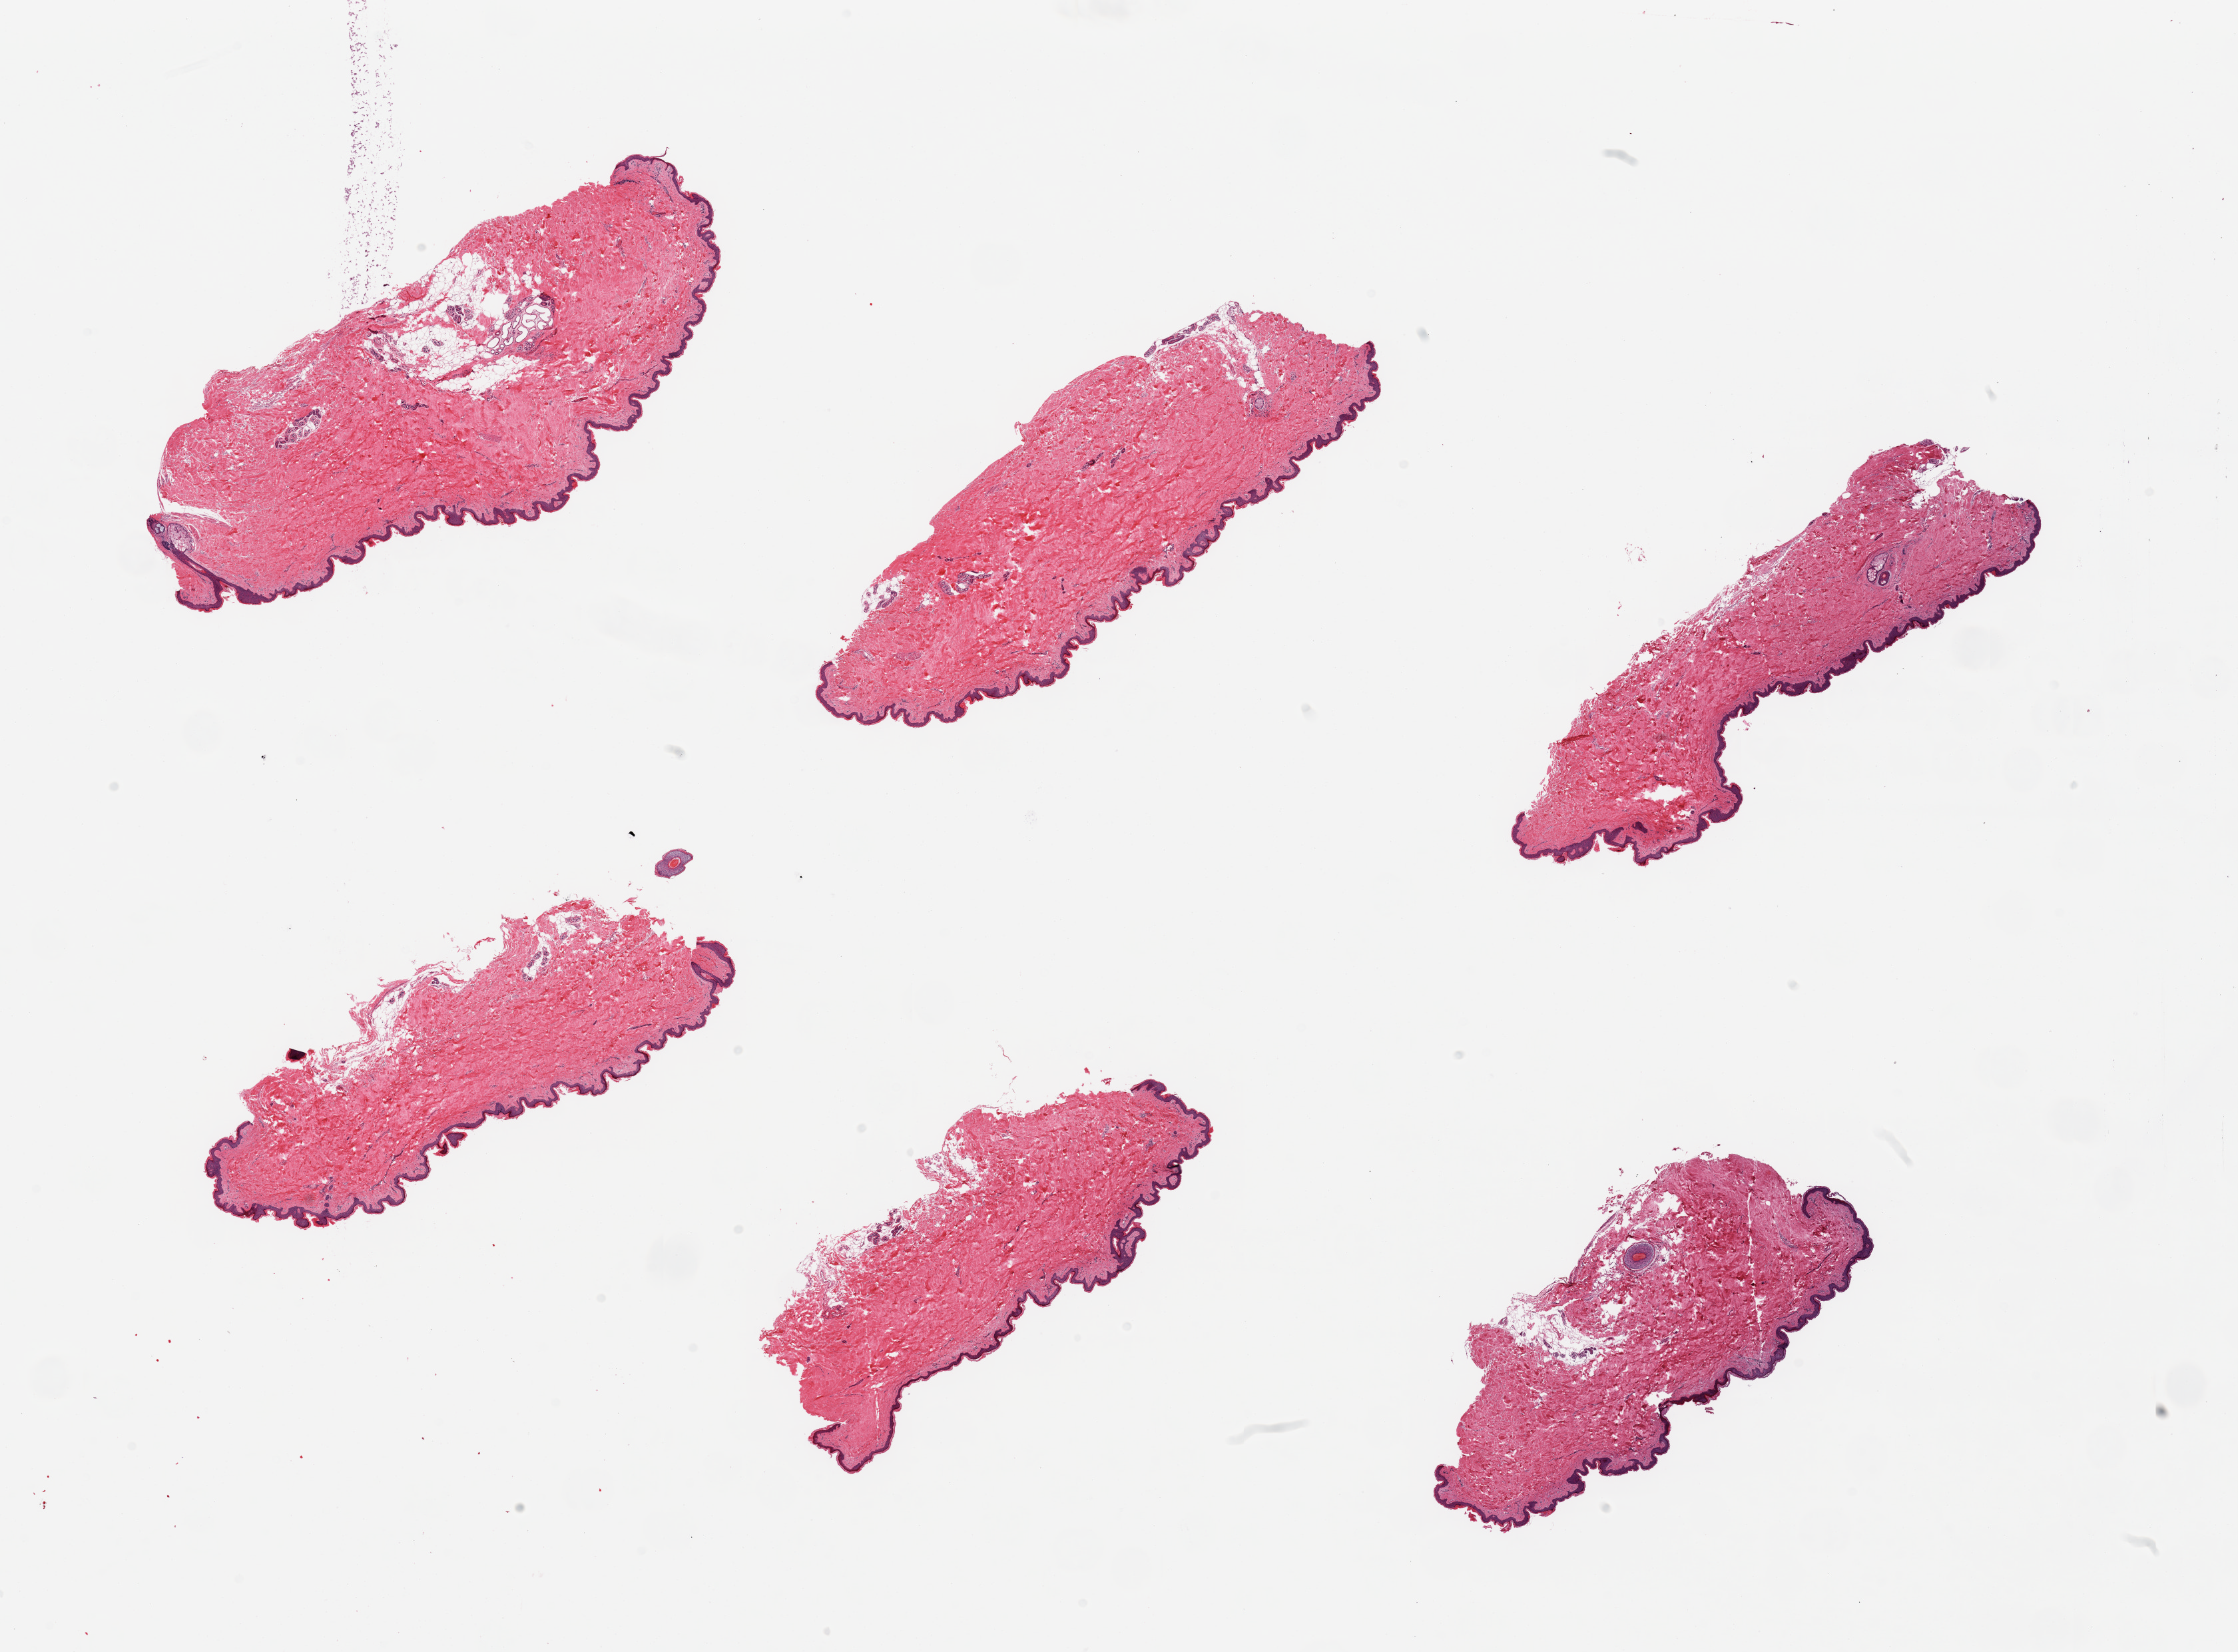
Digitized H&E-stained section — low-resolution overview of the scanned area, about 26.6 x 19.6 mm; PAXgene-fixed paraffin-embedded (PFPE) section; sampled site (target tissue): skin of suprapubic region; tissue donor sample.
• reviewer comment on this tissue sample: 6 pieces, well trimmed, few sections include 5-10% internal fat